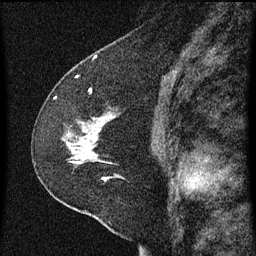
Breast MRI (dynamic contrast-enhanced), one sagittal slice; position 37 of 60 along the scan axis; dynamic contrast-enhanced series, image 2 of 3 at this slice position (ordered by acquisition); 1.5 T; TE 4.2 ms, TR 8 ms; 2 mm slice thickness; 256 × 256 image matrix, field of view 180 × 180 mm. Female patient, age 47 years.
Structures marked on this image (semi-automatically segmented with operator editing):
- analysis volume of interest (the breast-tissue region the enhancement analysis was run in; not a lesion): bounding box [x1, y1, x2, y2] px = [36, 102, 158, 213]
- tumour enhancement mask (voxels above the 70 % enhancement threshold inside the analysis volume of interest): [67, 116, 109, 179]